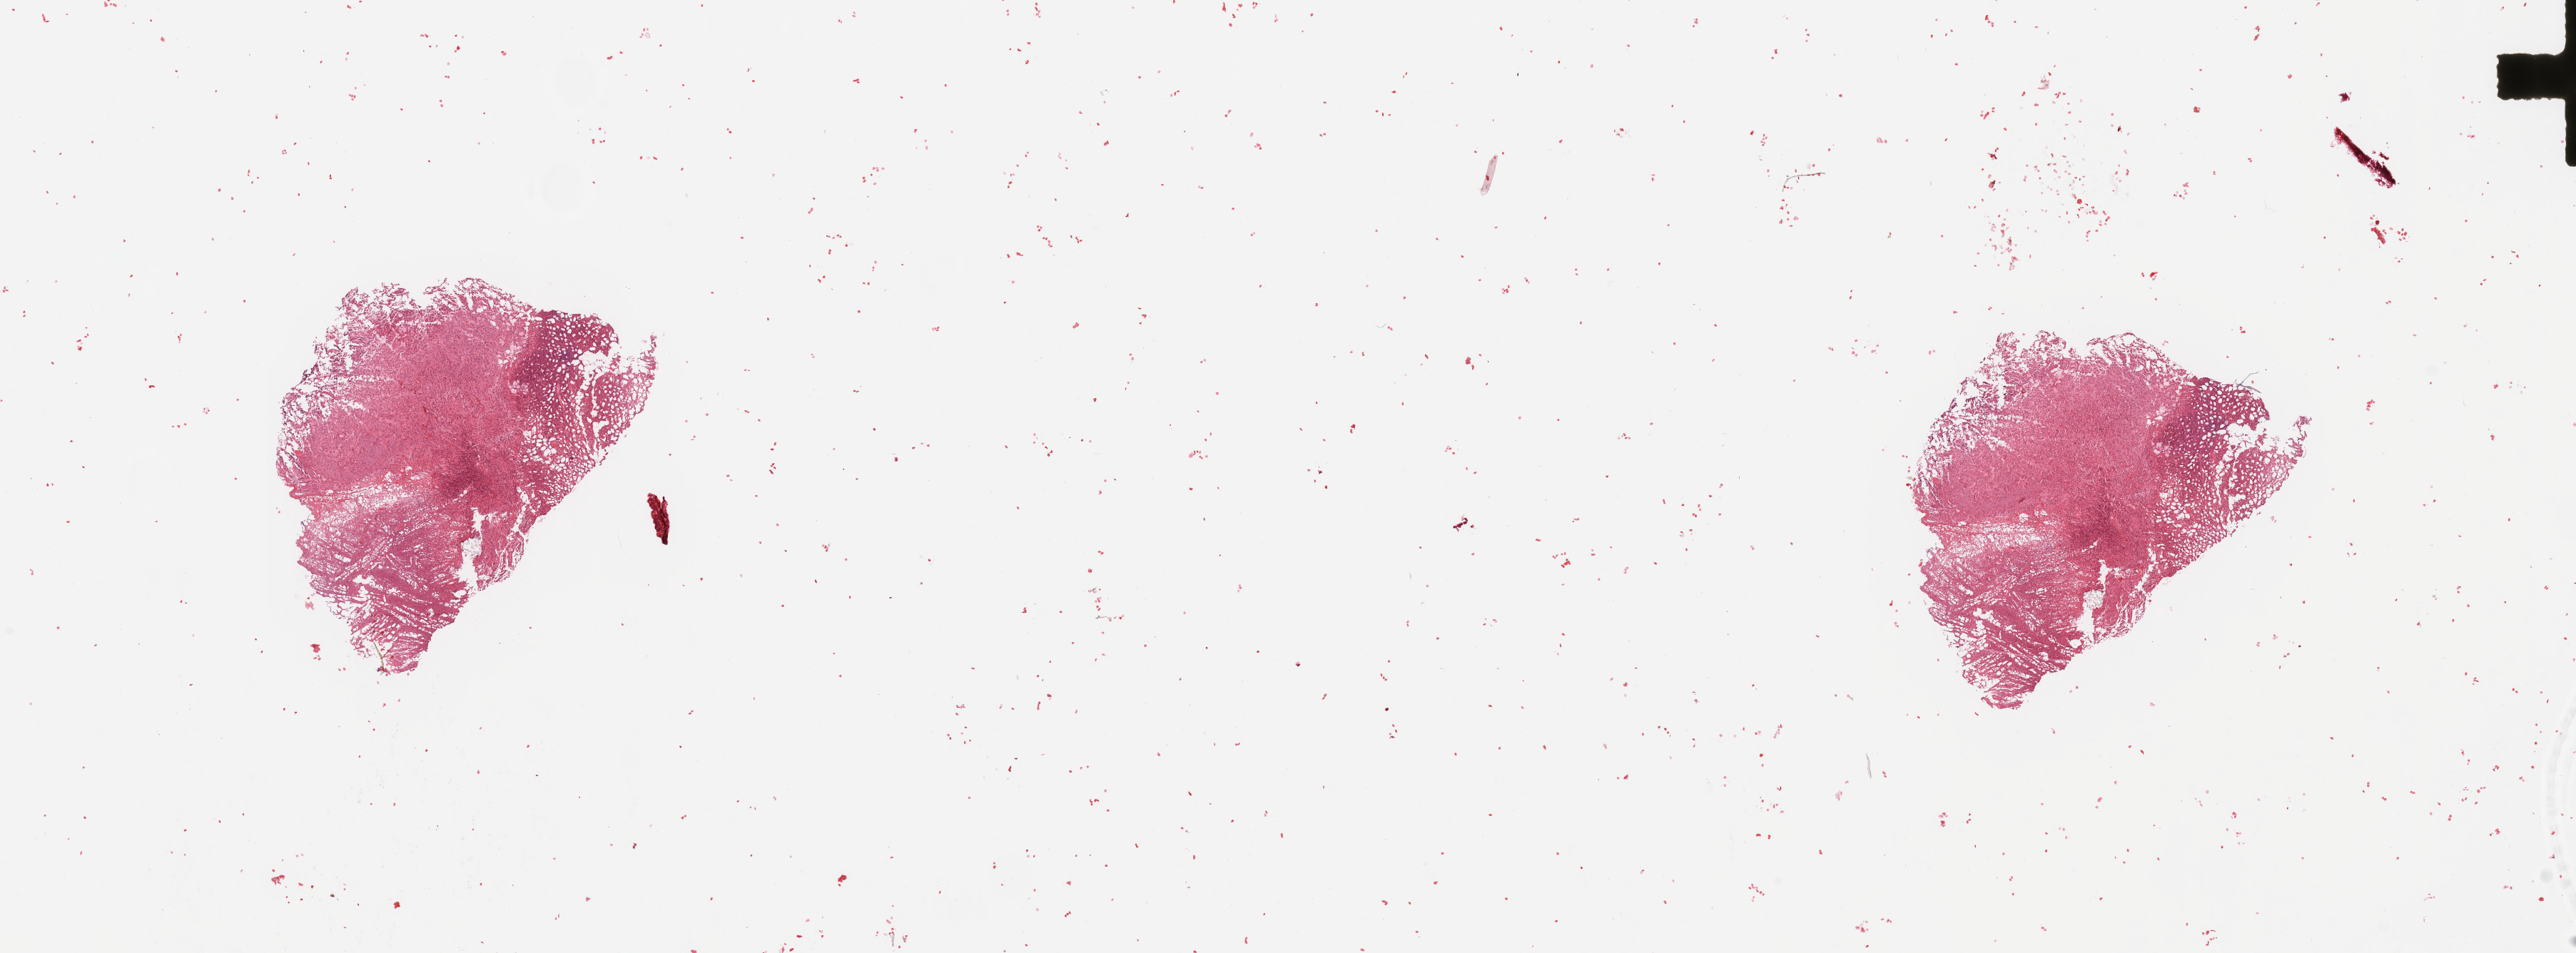
Digitized H&E tissue section (whole slide), whole scanned area (about 28.5 x 10.6 mm) shown as a low-resolution overview. Tumour tissue sample, sampled site: brain. Patient: female, age 68 years. Slide review estimates, as recorded: tumour nuclei 90%, necrosis 10%.
Primary tumour site (as recorded): temporal lobe. Diagnosis: Glioblastoma.